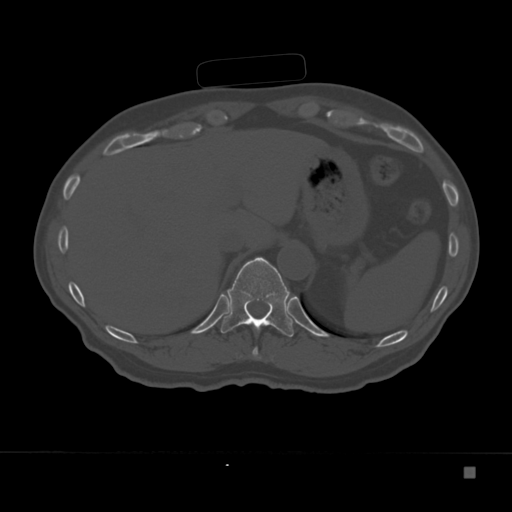
CT including the spine, one axial slice; position 156 of 332 along the scan axis; reconstruction kernel Br40s; 120 kVp; bone window (W 1800 / L 400 HU); 1.5 mm slice thickness; 512 × 512 image matrix, field of view 389 × 389 mm. Male patient, age 72 years. From the clinical record (not read from this slice): primary cancer: skeletal.
Outlined on this slice (semi-automatically segmented with operator editing):
- T10 vertebra: bounding box <252,347,258,356> (left, top, right, bottom; pixels)
- T11 vertebra: <220,257,294,337>